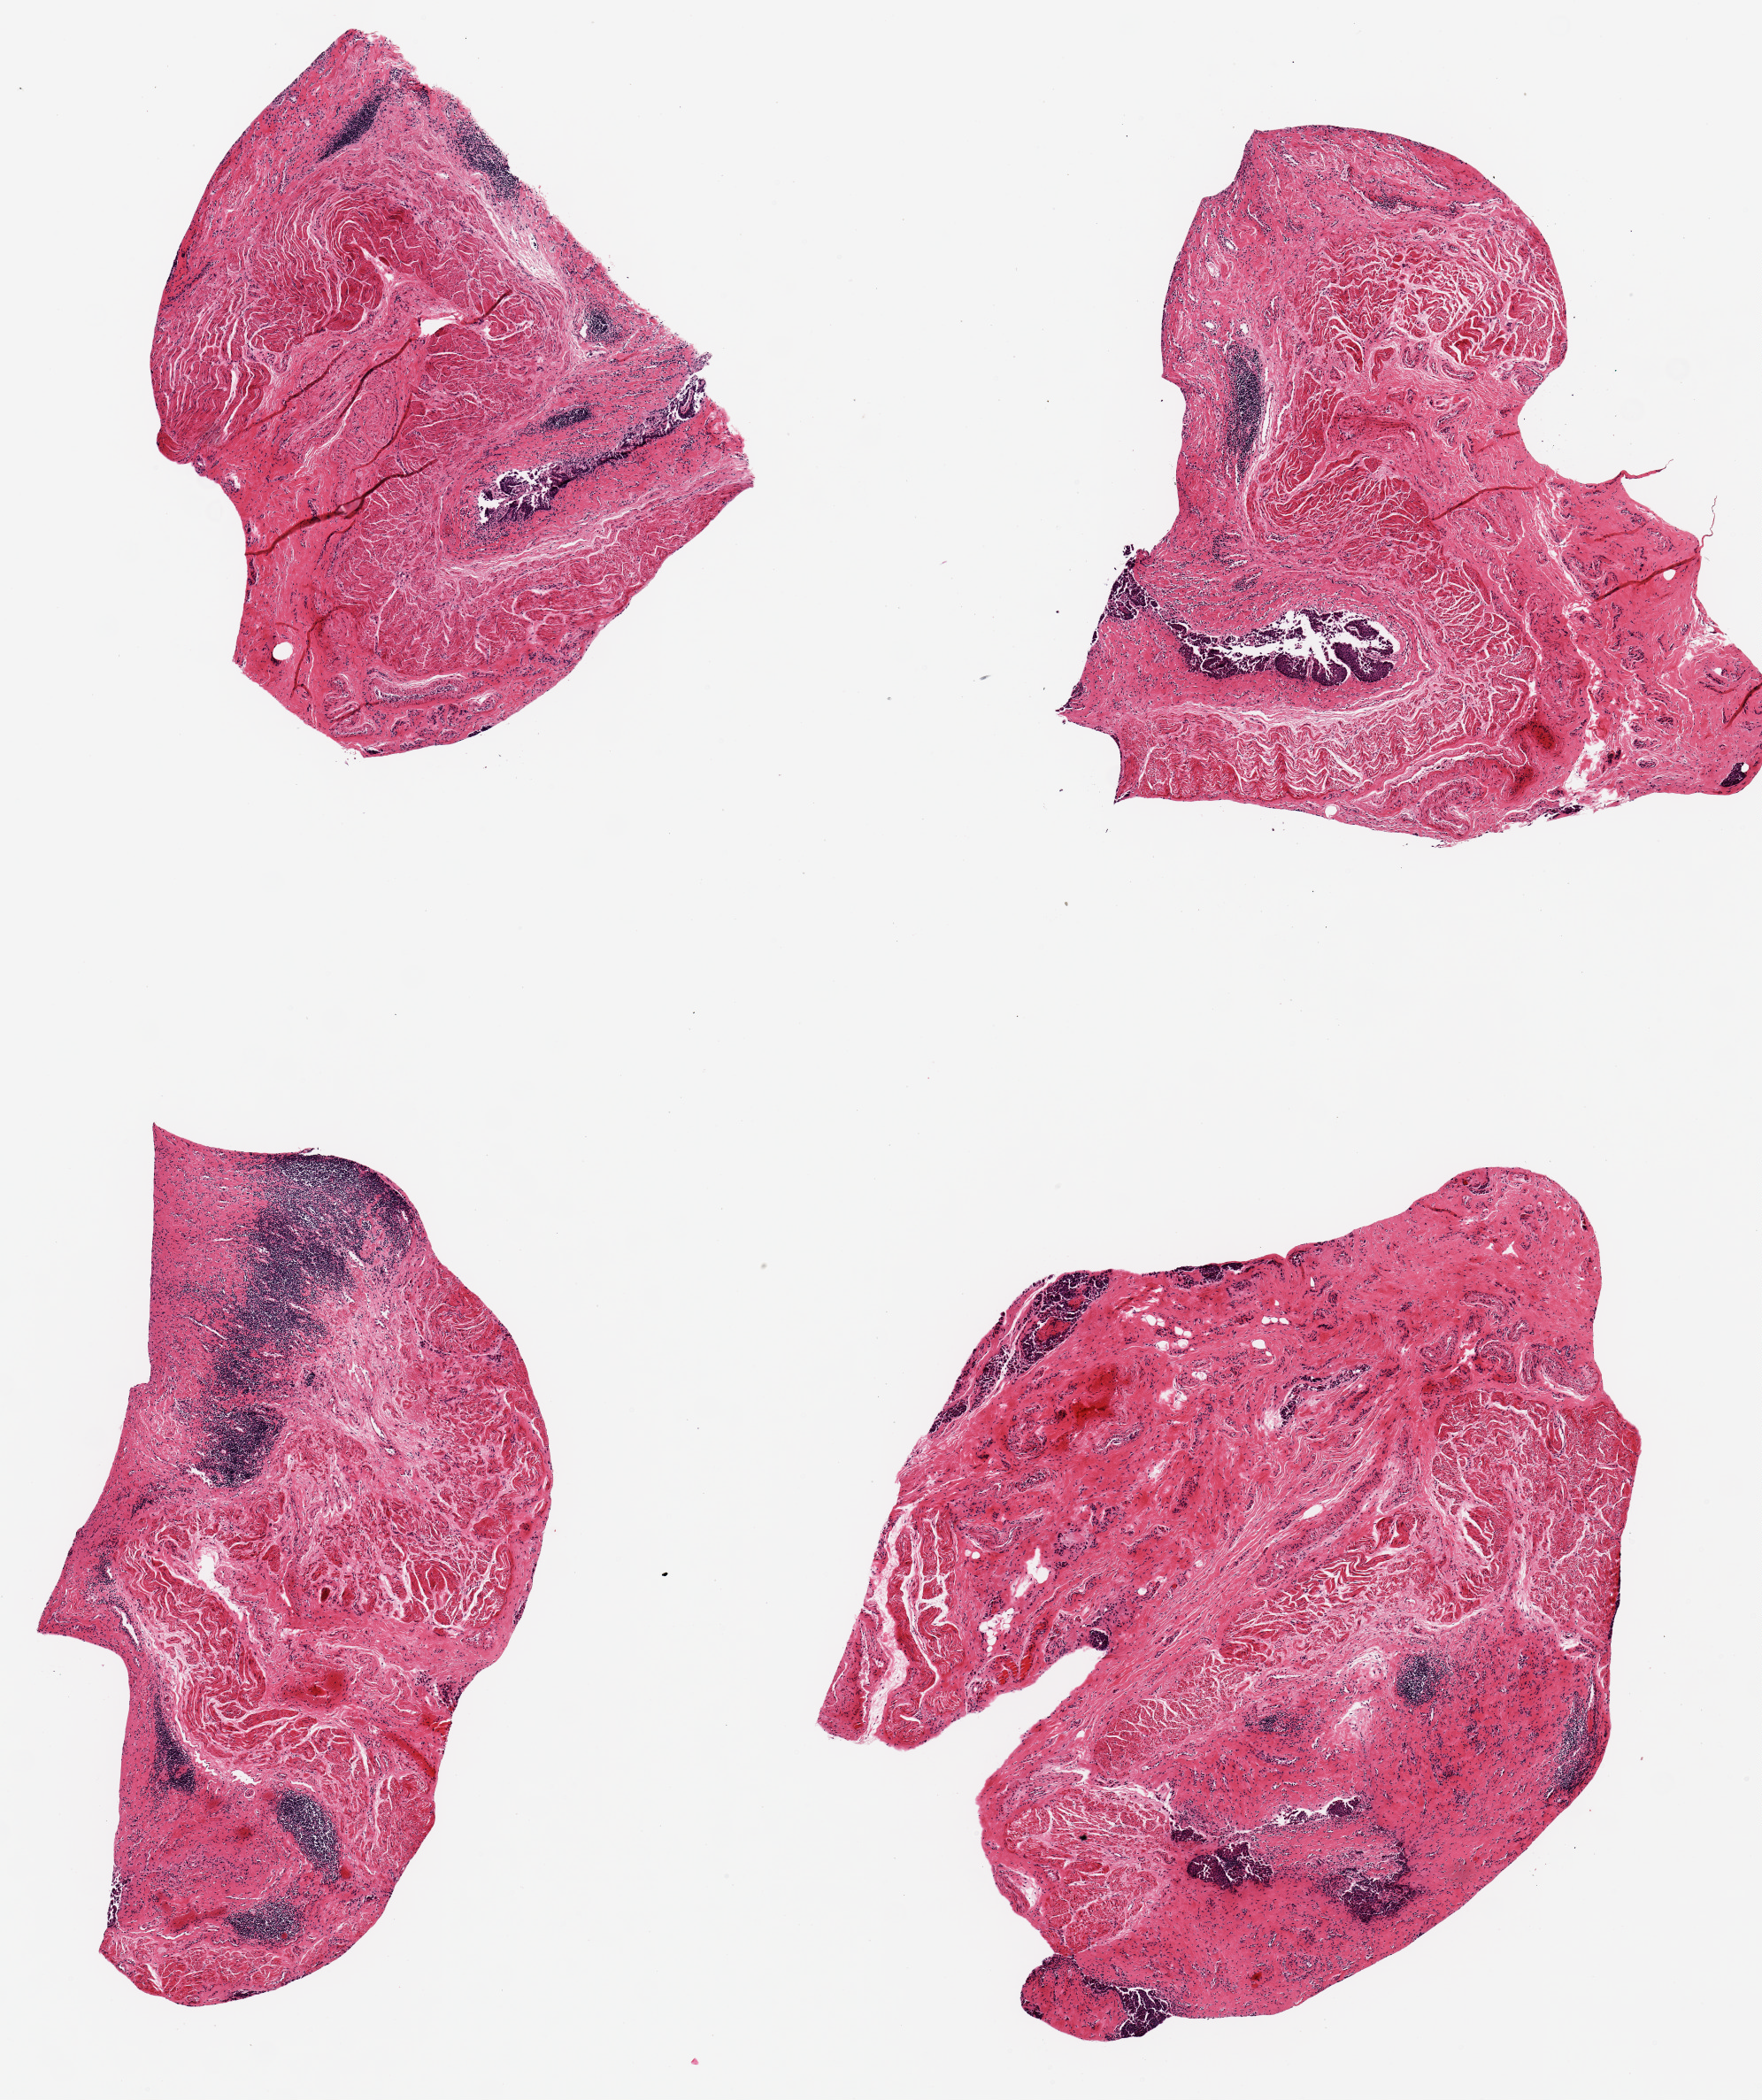
Whole-slide image, H&E stain, brightfield — shown as a low-resolution overview of the whole scanned area (about 7.9 x 9.4 mm, acquisition: 20x scan). PAXgene-fixed, paraffin-embedded tissue. Target tissue: esophageal mucous membrane. Tissue donor sample. Donor: male.
Pathologist's review note for this sample: 4 pieces, up to 4x3mm; mucosa unusually autolyzed; thick muscularis mucosae; chronic inflammation.